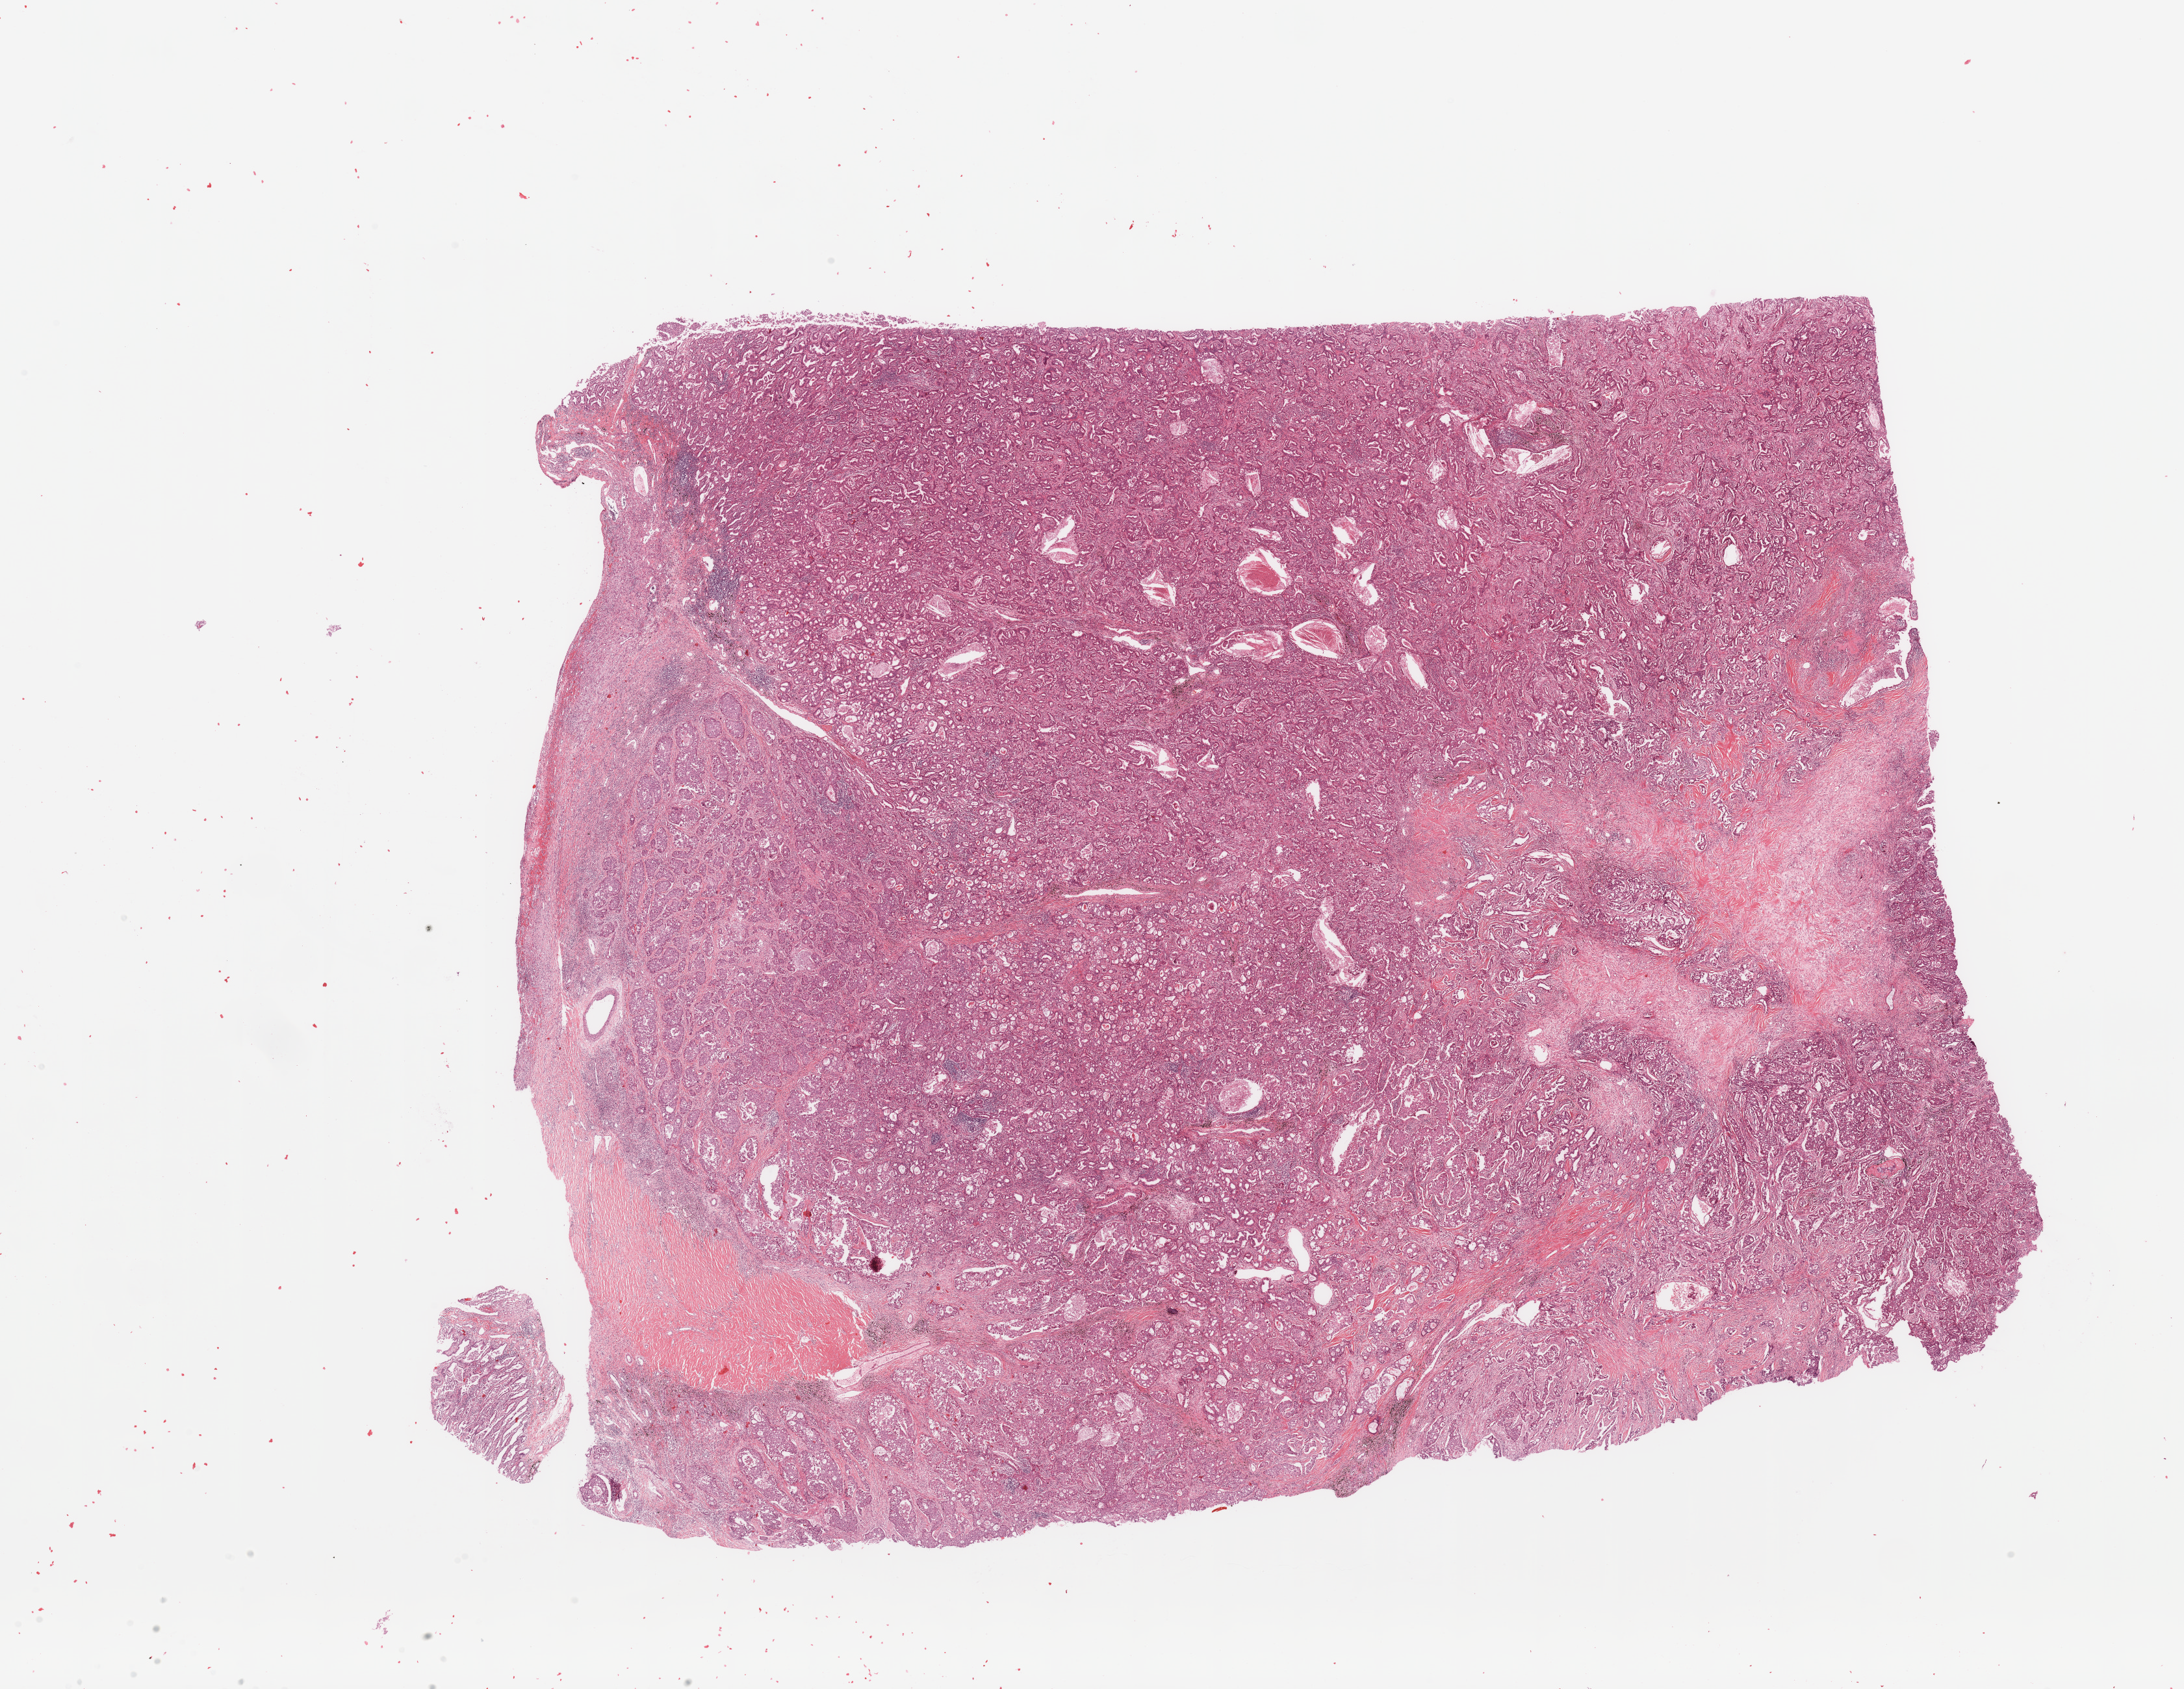
Whole-slide histology image, H&E-stained, whole scanned area (about 26.6 x 20.6 mm, acquisition: 20x scan) shown as a low-resolution overview. Tumour tissue sample, lung. 54-year-old female patient. Histologic grade: G2 (moderately differentiated).
- diagnosis: Adenocarcinoma, NOS
- AJCC pathologic stage: IIIA